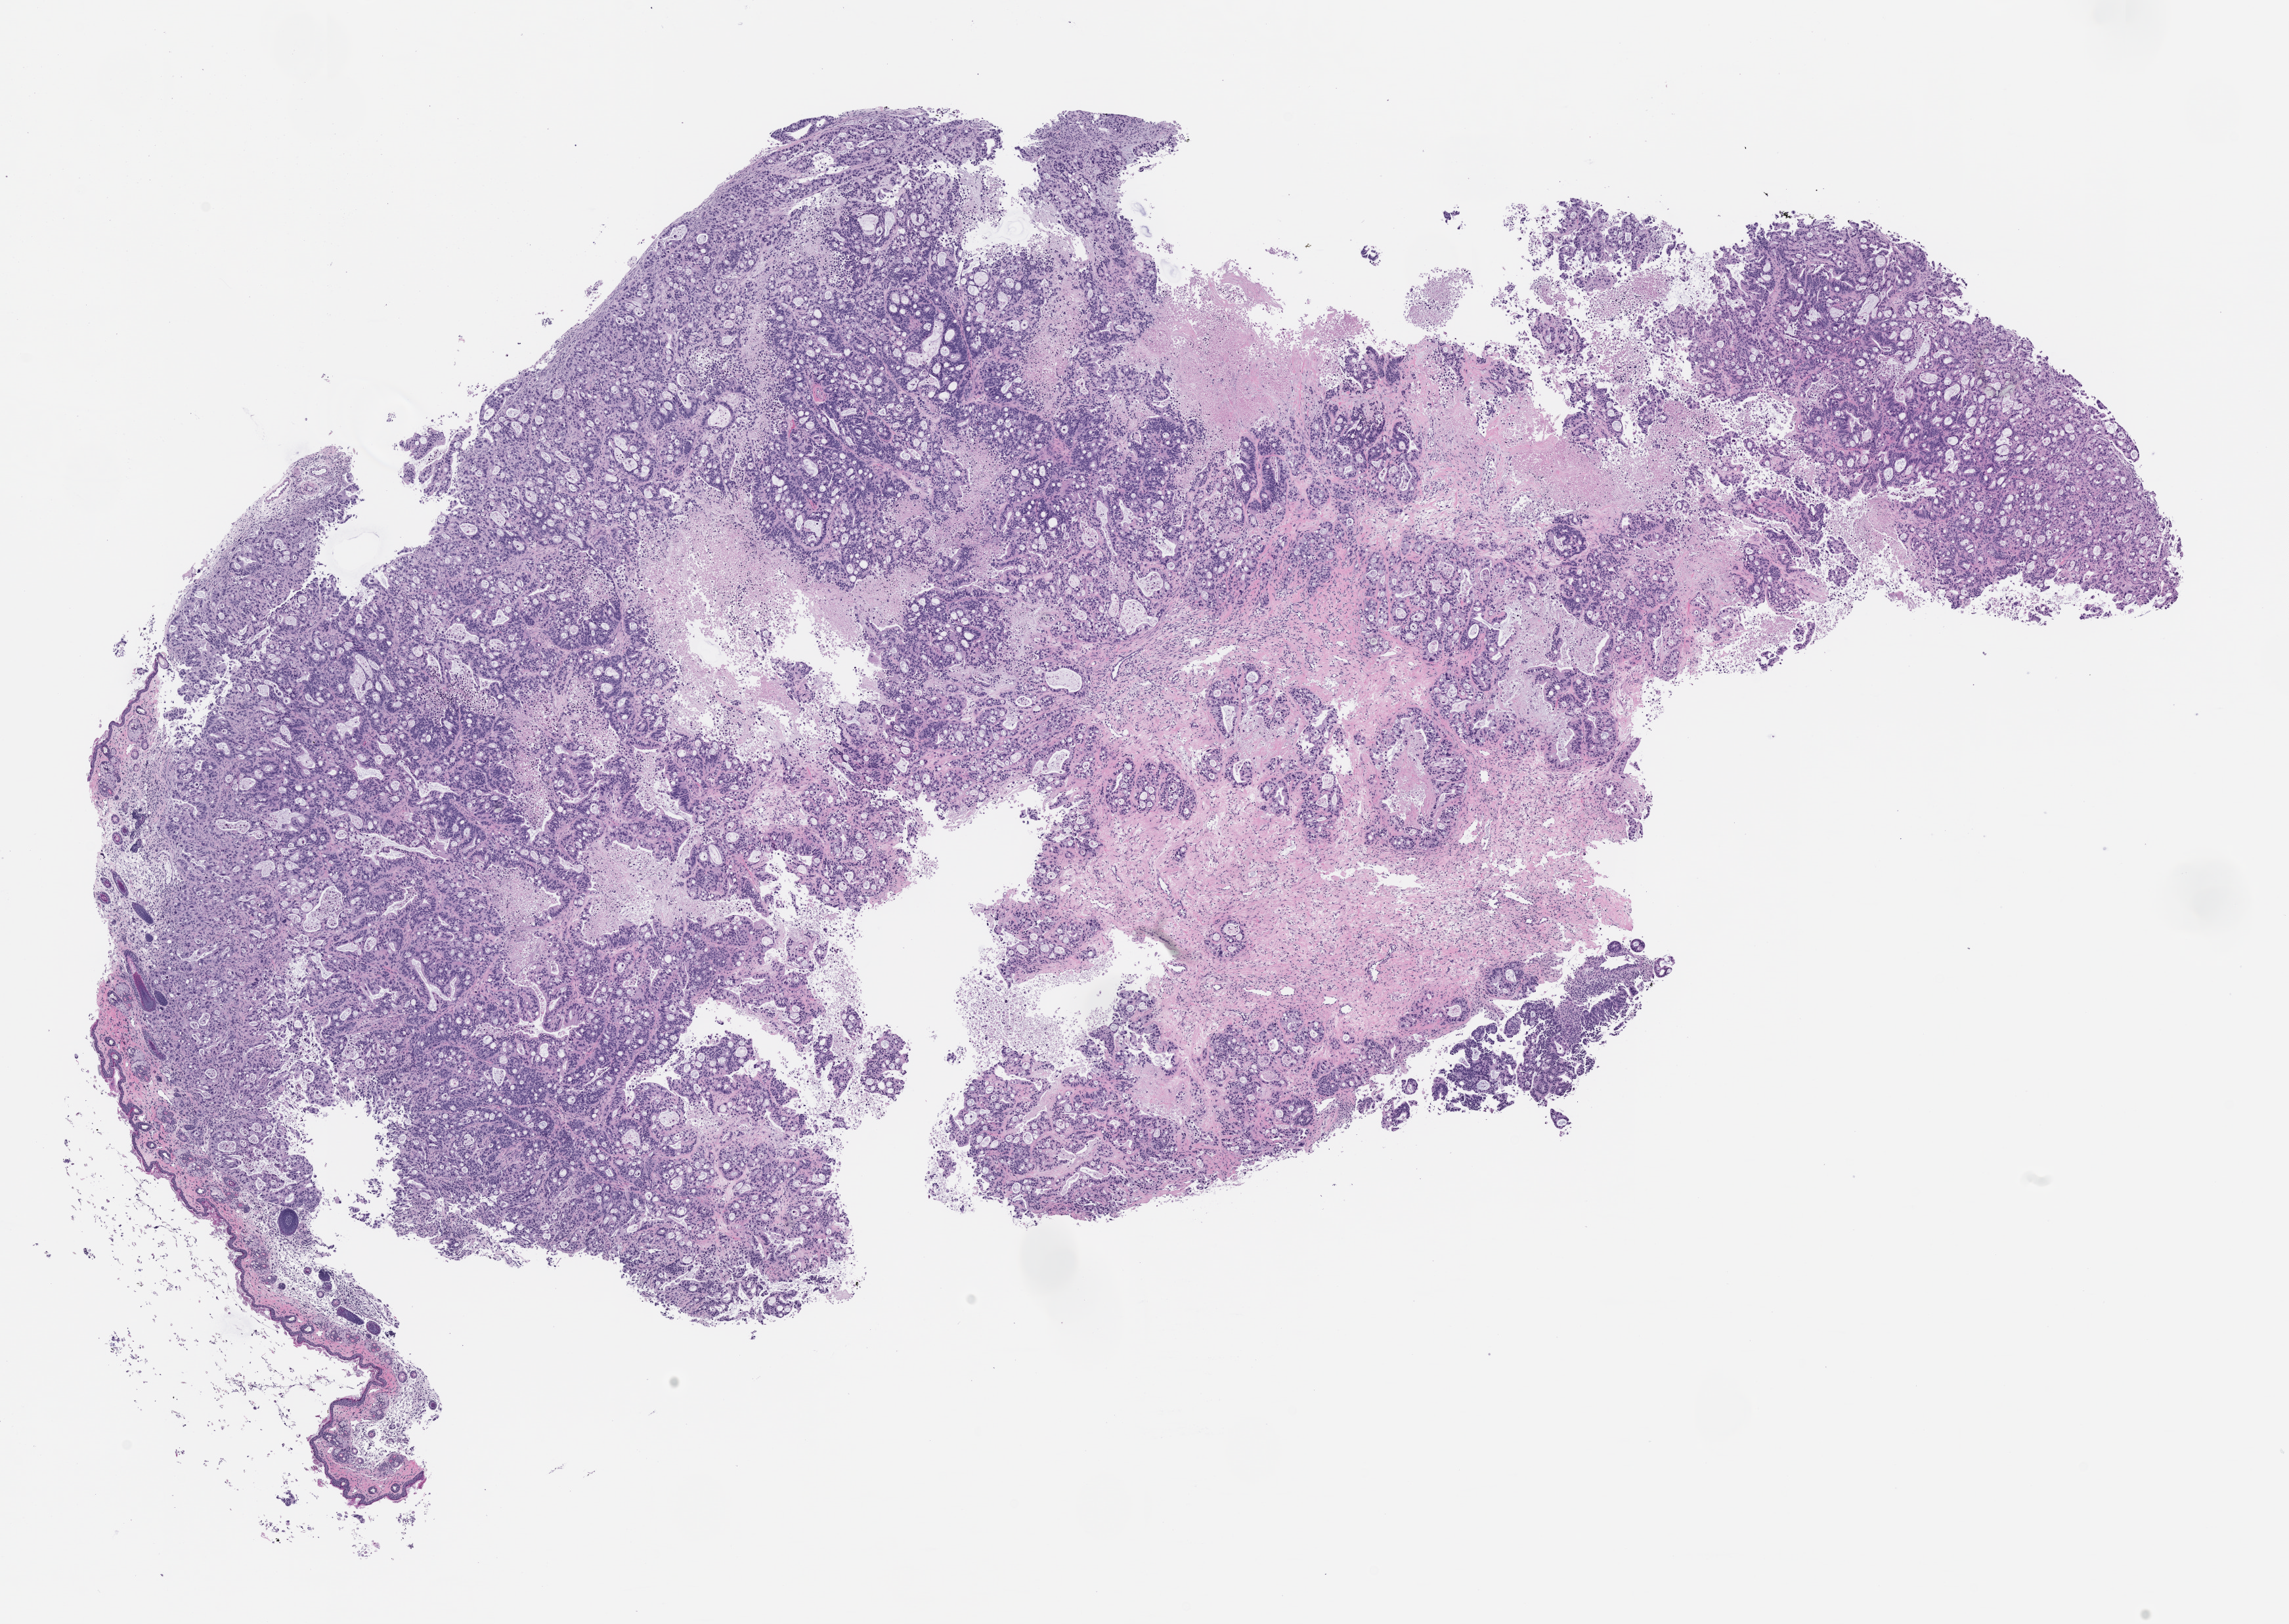
Whole-slide image, hematoxylin and eosin (H&E): patient-derived xenograft (human tumor grown in a mouse), passage 1, shown as a low-resolution overview of the whole scanned area (about 14.0 x 9.9 mm), formalin-fixed paraffin-embedded section, originating tumor site category: pancreas.
• originating patient diagnosis: Pancreatic Adenocarcinoma